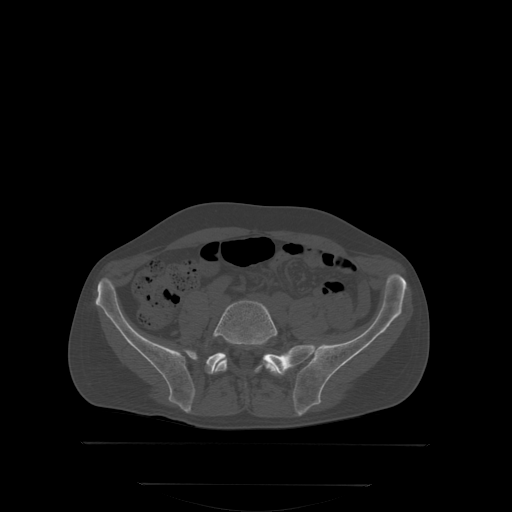
CT including the spine, one axial slice; position 91 of 350 along the scan axis; bone window (W 1800 / L 400 HU); 512 × 512 image matrix. Male patient, age 58 years. Case-level facts recorded for this patient, not image findings: primary cancer: prostate.
Outlined on this slice (semi-automatically segmented with operator editing):
- L5 vertebra: bounding box (x1, y1, x2, y2) in pixels: (214, 300, 279, 385)